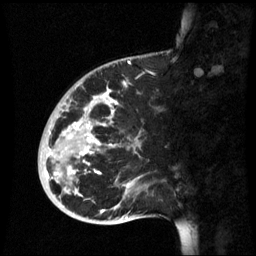
Breast MRI (dynamic contrast-enhanced), one sagittal slice. Dynamic contrast-enhanced series, image 2 of 3 at this slice position (ordered by acquisition). 1.5 T. TE 4.2 ms, TR 8.9 ms. 2.6 mm slice thickness. 256 × 256 image matrix, field of view 220 × 220 mm. Female patient, age 35 years. Case-level facts recorded for this patient, not image findings: setting: breast cancer imaged before/during neoadjuvant chemotherapy; receptor status: HR-positive, HER2-negative.
Annotated regions visible in this slice (semi-automatically segmented with operator editing):
- analysis volume of interest (the breast-tissue region the enhancement analysis was run in; not a lesion): bounding box <38,74,155,221> (left, top, right, bottom; pixels)
- tumour enhancement mask (voxels above the 70 % enhancement threshold inside the analysis volume of interest): <46,88,139,213>